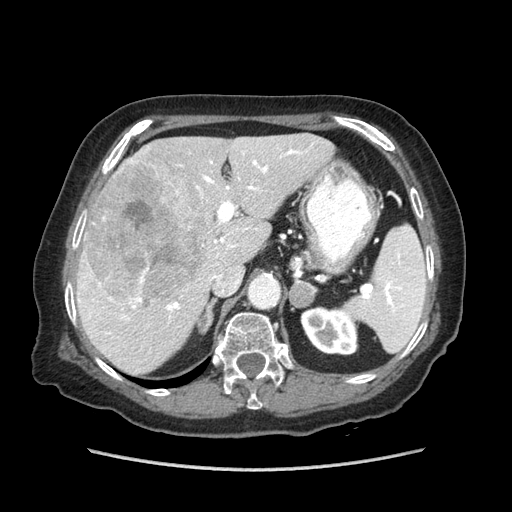
Contrast-enhanced abdominal CT (liver protocol), one axial slice; slice 50 of 89 in the series (ordered by position); soft-tissue window (W 400 / L 40 HU); 2.5 mm slice thickness; 512 × 512 image matrix, field of view 360 × 360 mm. From the clinical record (not read from this slice): diagnosis: hepatocellular carcinoma (patient treated with transarterial chemoembolisation; whether this scan precedes or follows treatment is not stated here); TNM stage (as recorded): Stage-IIIA.
Structures marked on this image (semi-automatic segmentation, software-assisted and operator-edited):
- liver parenchyma outside the tumour (the mass and vessels are separate outlines, so this box may not span the whole liver): bounding box (x1, y1, x2, y2) in pixels: (76, 134, 334, 374)
- mass: (85, 159, 206, 297)
- liver vessels: (78, 144, 313, 334)